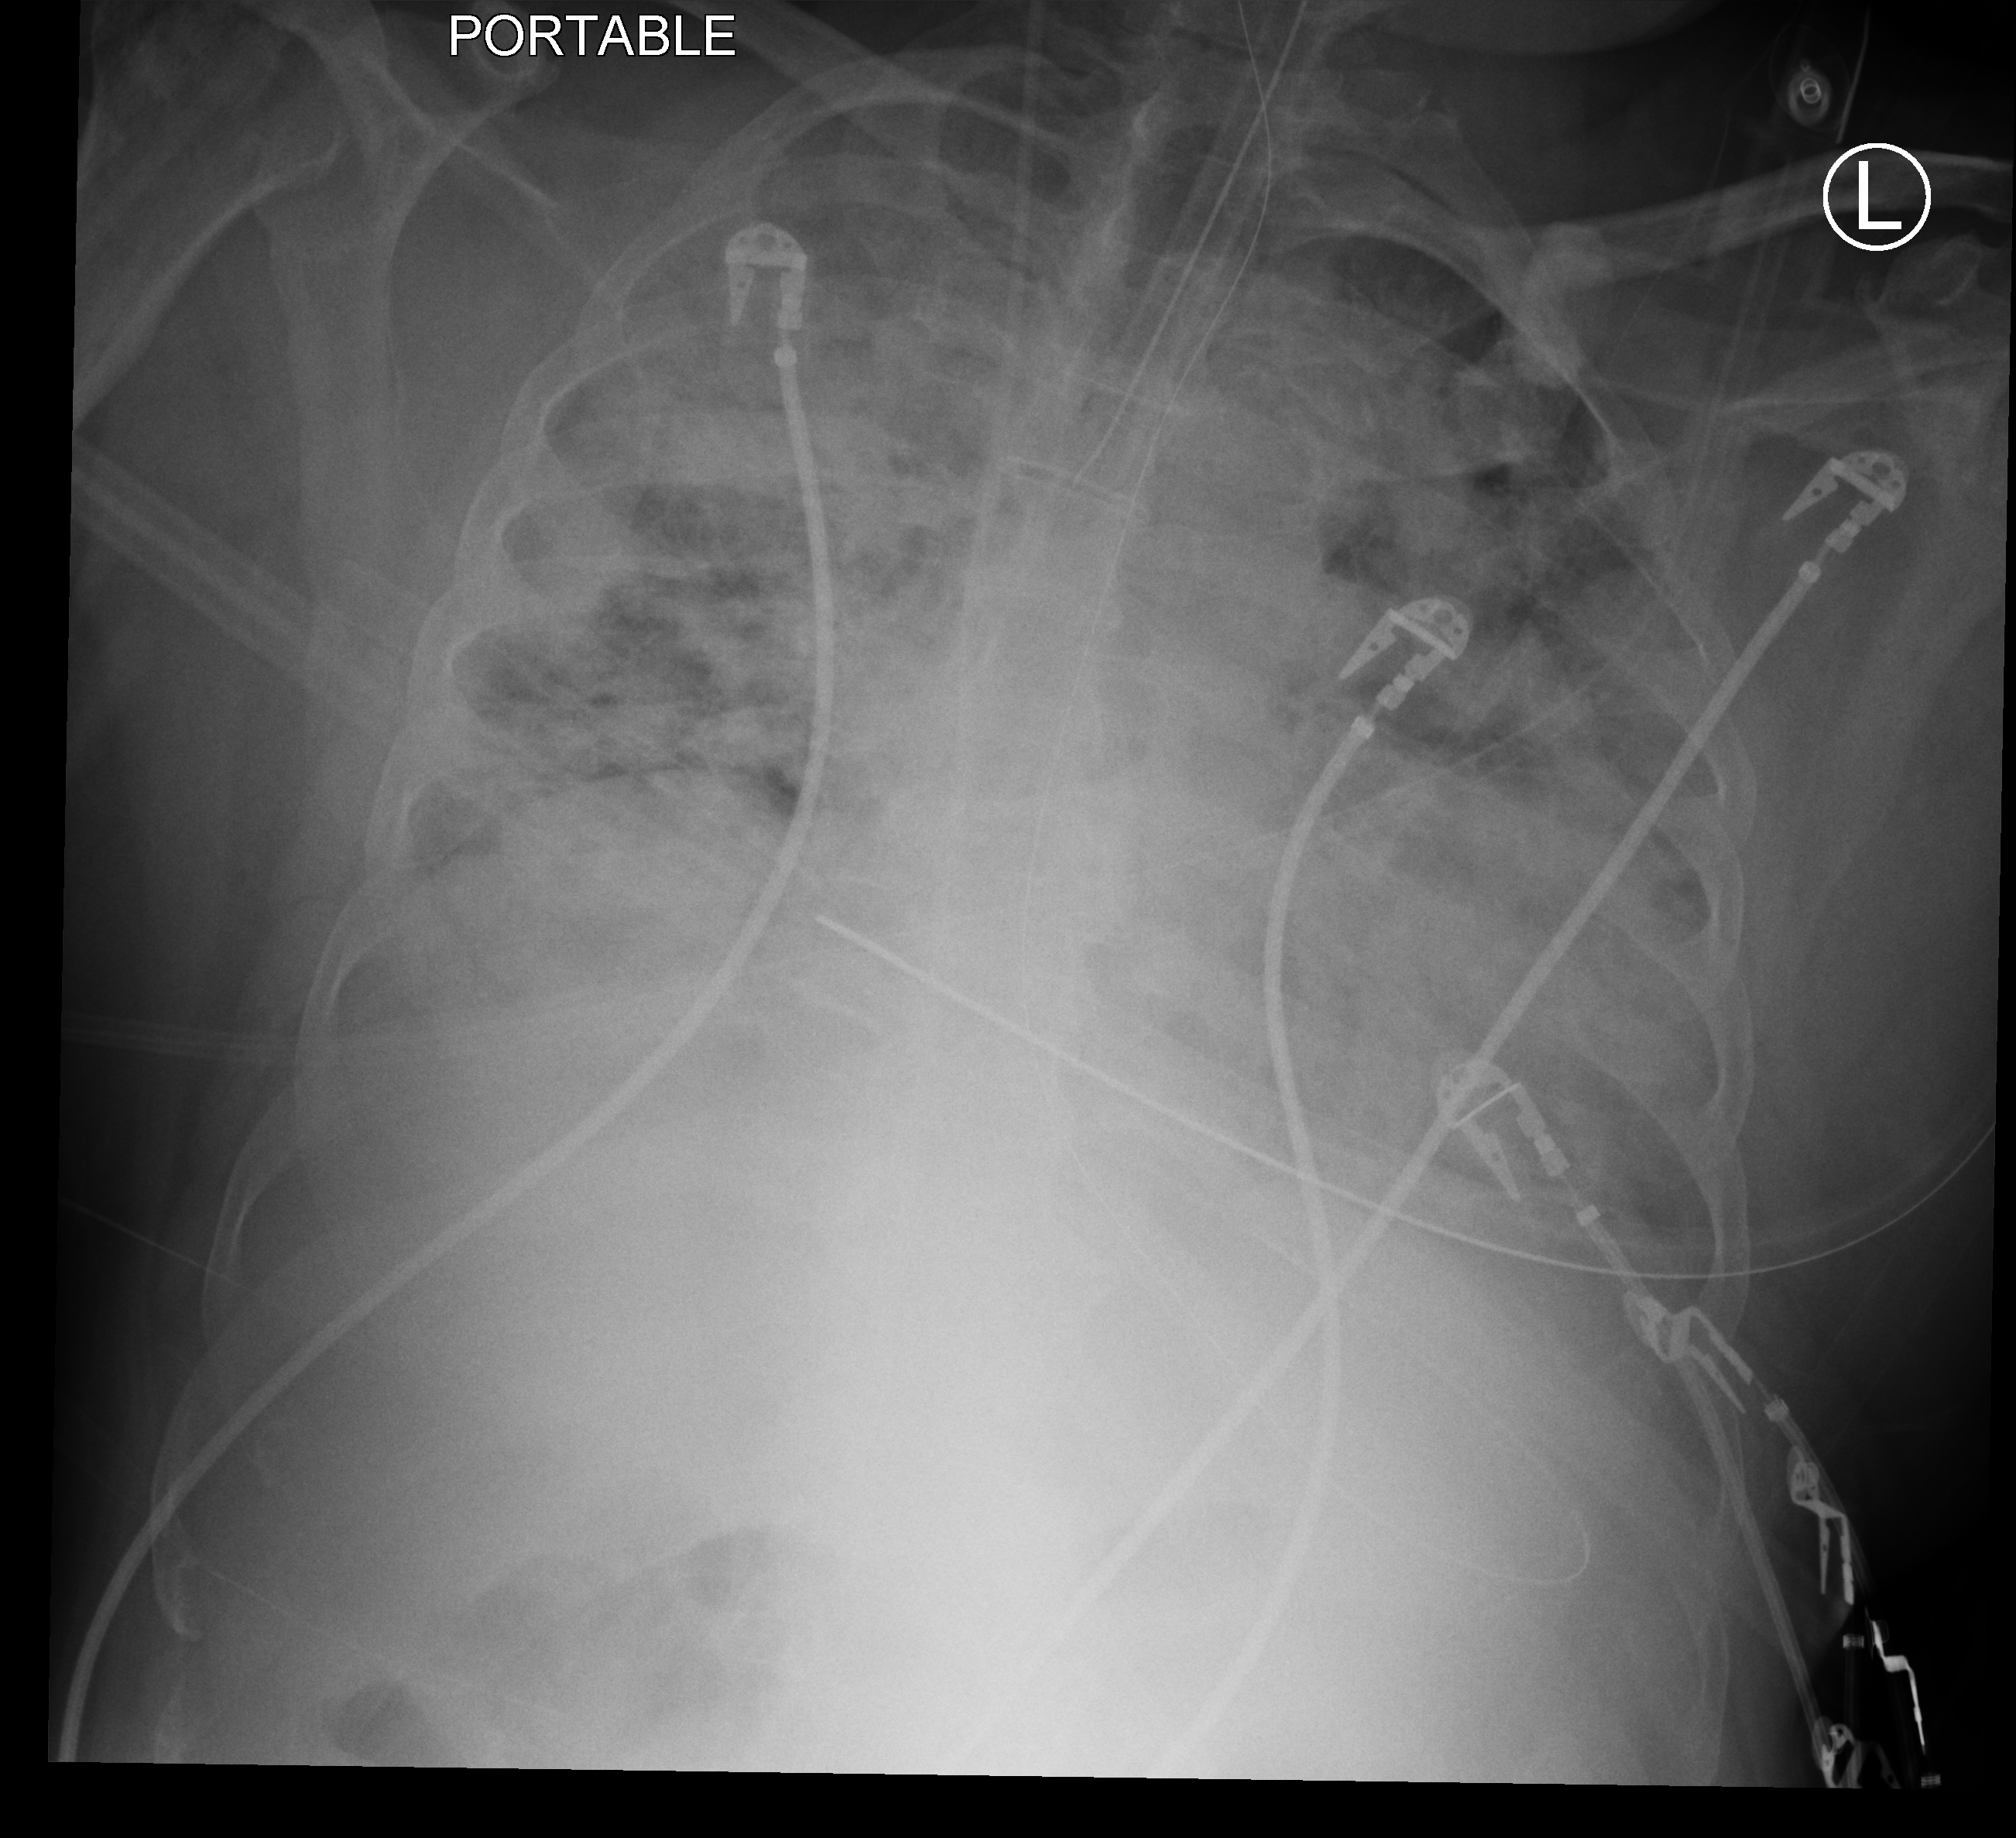
Portable chest radiograph; anteroposterior (AP) projection. Patient hospitalised with COVID-19; male, aged 60–74 years.
From the hospital-stay record, not from the radiograph (when in the stay this image was taken is not recorded): diabetes (admission record): no; COPD (admission record): no; admitted to intensive care during this hospital stay: yes.